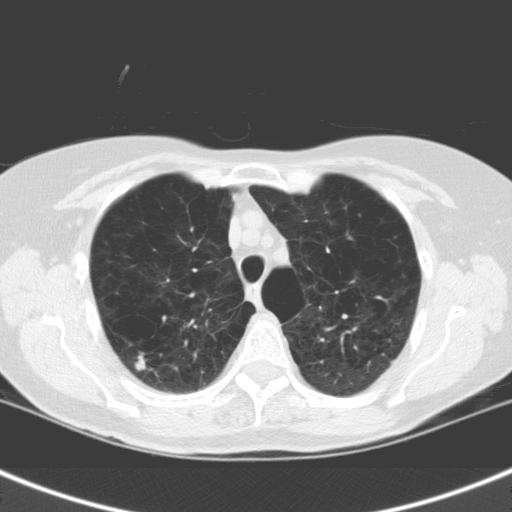
Low-dose screening chest CT, axial slice; second annual screen; lung window (W 1500 / L -600 HU); standard (soft-tissue) reconstruction kernel (C). Female, age 63 years at enrolment. Current smoker at enrolment.
Lesion marked by an expert reader, bounding box <116,340,161,387> (left, top, right, bottom; pixels). Reader record for this screening exam (exam-level; its link to the box is not recorded): non-calcified nodule or mass ≥4 mm, right upper lobe, 7 × 7 mm, spiculated (stellate) margins, soft tissue attenuation, pre-existing on the prior screen: no. Official screen result: positive, other. Lung cancer was diagnosed 228 days after this screen: squamous cell carcinoma, NOS, right upper lobe, moderately differentiated (G2), stage IA (AJCC 6th edition), 14 mm at pathology.